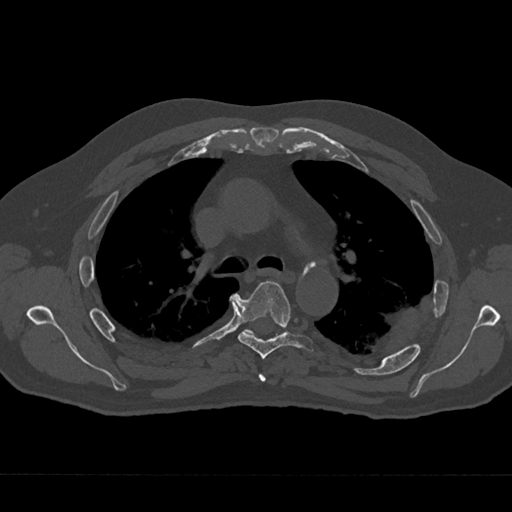
CT including the spine, one axial slice; position 471 of 797 along the scan axis; reconstruction kernel Br40s/3; bone window (W 1800 / L 400 HU); 512 × 512 image matrix, field of view 377 × 377 mm. Patient: male, 75 years. From the clinical record (not read from this slice): primary cancer: renal; vertebrae with lytic lesions (as recorded): T4.
Outlined on this slice (semi-automatically segmented with operator editing):
- T4 vertebra: box from (x=259, y=374) to (x=266, y=382) px
- T5 vertebra: (x=236, y=281)–(x=314, y=359)
- T6 vertebra: (x=244, y=329)–(x=254, y=335)